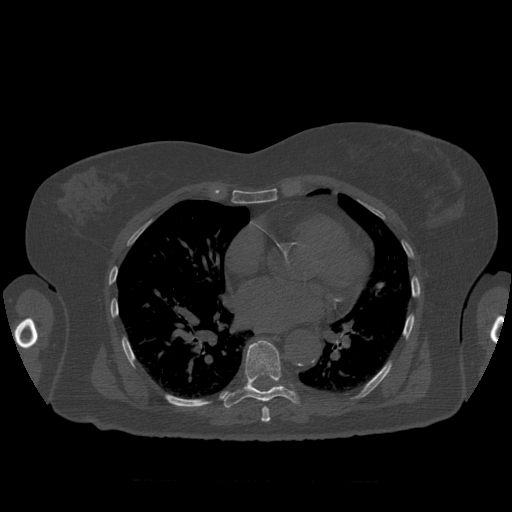
CT including the spine, one axial slice. Slice 379 of 399 in the series (ordered by position). Bone window (W 1800 / L 400 HU). 1.25 mm slice thickness. 512 × 512 image matrix, field of view 404 × 404 mm. Patient age 81 years. From the clinical record (not read from this slice): primary cancer: renal; vertebrae with lytic lesions (as recorded): L1.
Structures marked on this image (semi-automatic segmentation, software-assisted and operator-edited):
- T7 vertebra: box from (x=261, y=406) to (x=271, y=422) px
- T8 vertebra: (x=223, y=341)–(x=300, y=408)